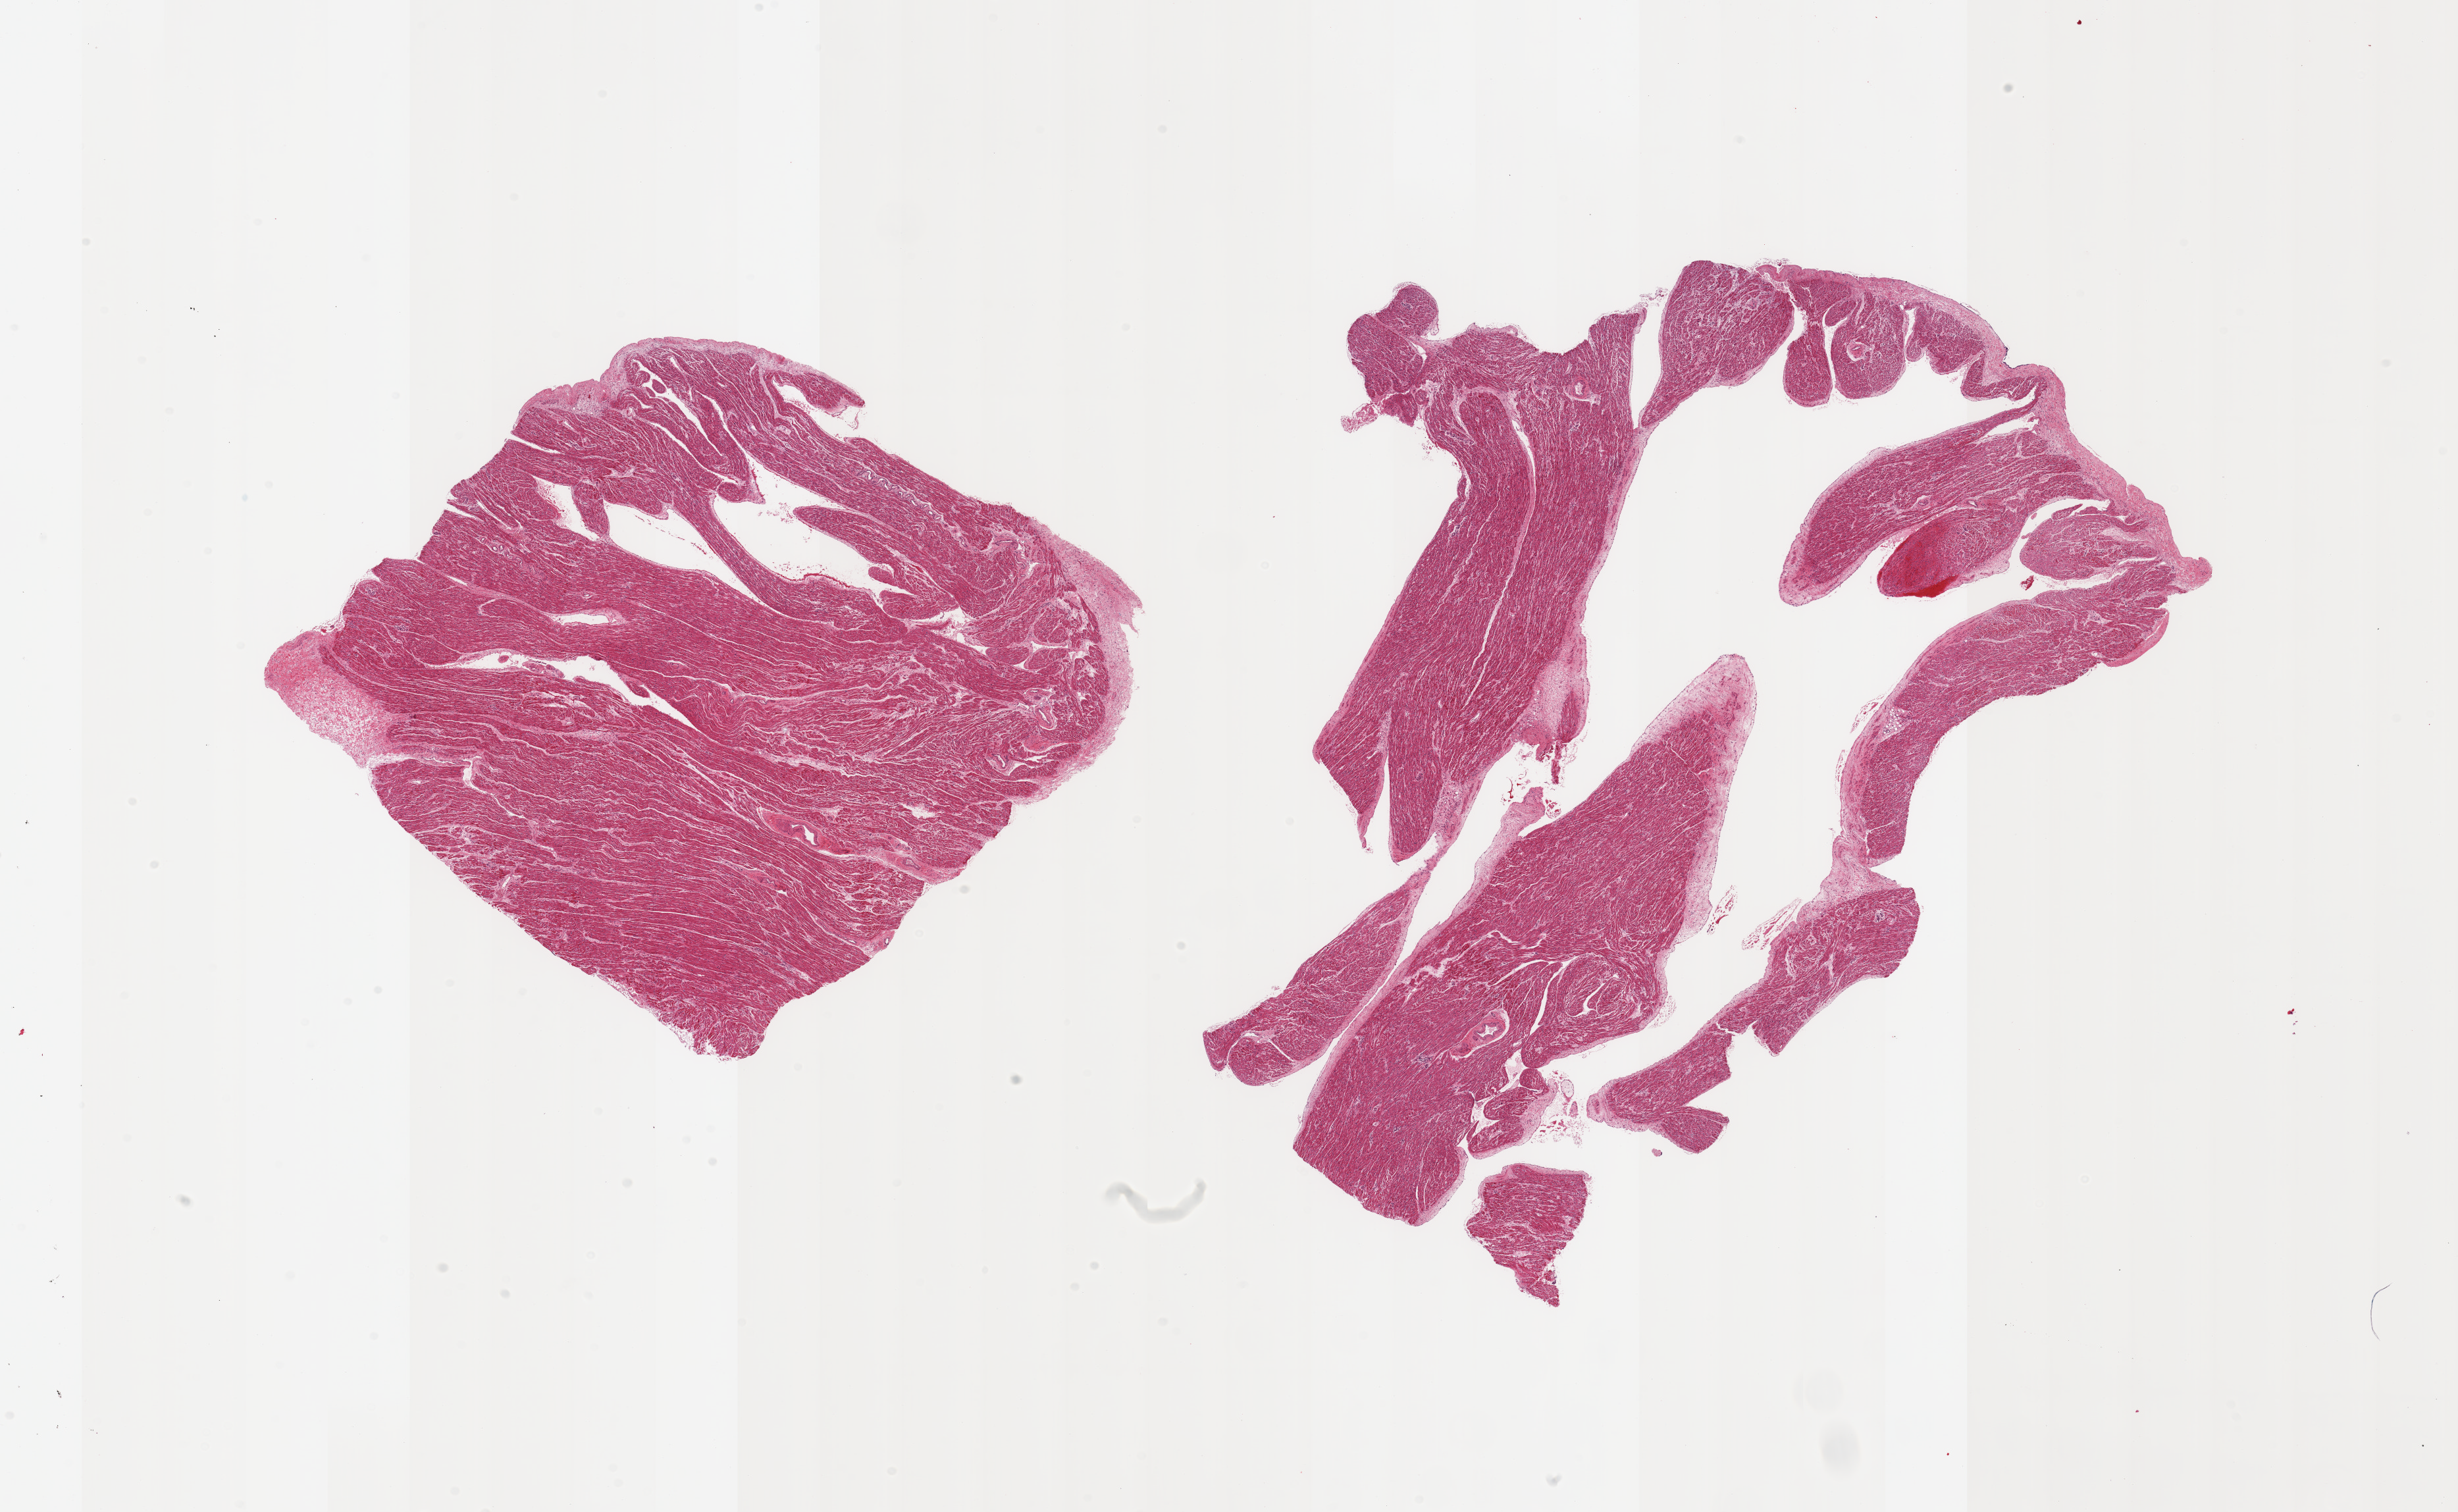
Haematoxylin and eosin whole-slide image, a low-resolution overview of the entire scanned area, about 29.5 x 18.2 mm (from a 20x scan); PAXgene-fixed, paraffin-embedded tissue; section of auricular appendage (target tissue); tissue donor sample.
Pathologist's review note for this sample: 2 pieces.